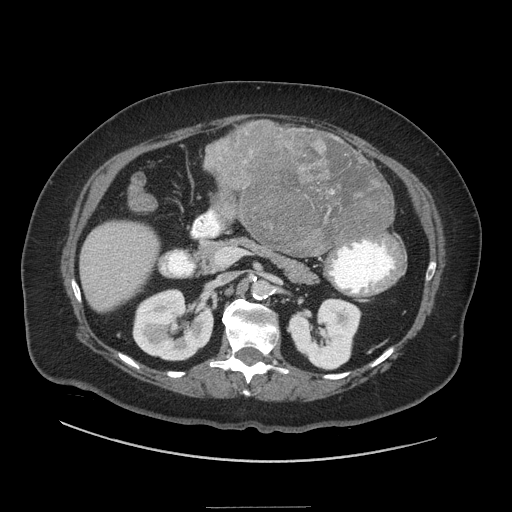
Contrast-enhanced abdominal CT (liver protocol), one axial slice; slice 10 of 81 in the series (ordered by position); reconstruction kernel STANDARD; soft-tissue window (W 400 / L 40 HU); 512 × 512 image matrix, field of view 440 × 440 mm. Case-level facts recorded for this patient, not image findings: diagnosis: hepatocellular carcinoma (patient treated with transarterial chemoembolisation; whether this scan precedes or follows treatment is not stated here); TNM stage (as recorded): Stage-II; Child-Pugh class: A.
Outlined on this slice (semi-automatically segmented with operator editing):
- liver parenchyma outside the tumour (the mass and vessels are separate outlines, so this box may not span the whole liver): box from (x=80, y=122) to (x=394, y=310) px
- mass: (x=205, y=121)–(x=394, y=255)